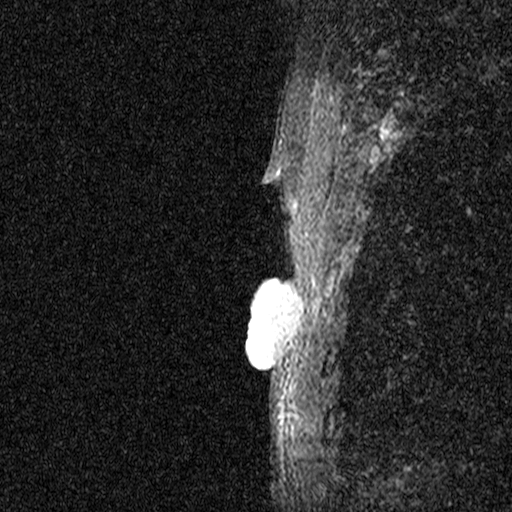
Breast MRI (dynamic contrast-enhanced), one sagittal slice. Slice 41 of 44 in the series (ordered by position). Dynamic contrast-enhanced study with each time point stored as its own series, time point 2 of 3 at this slice position (early post-contrast, ordered by acquisition time). 1.5 T. TE 4.5 ms, TR 11 ms. 2.05 mm slice thickness. 512 × 512 image matrix, field of view 200 × 200 mm. Female patient, age 44 years. Case-level facts recorded for this patient, not image findings: setting: breast cancer imaged before/during neoadjuvant chemotherapy; receptor status: HR-positive, HER2-negative.
Structures marked on this image (semi-automatically segmented with operator editing):
- analysis volume of interest (the breast-tissue region the enhancement analysis was run in; not a lesion): bounding box (x1, y1, x2, y2) in pixels: (204, 254, 317, 401)
- tumour enhancement mask (voxels above the 90 % enhancement threshold inside the analysis volume of interest): (247, 259, 294, 379)